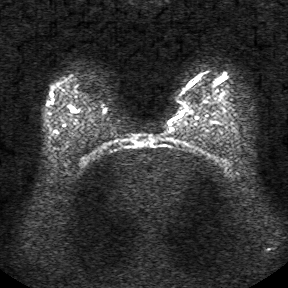
Breast MRI, one axial slice; diffusion-weighted series; image 2 of 4 stored at this slice position (different b-values; order by instance number); 1.5 T; 5 mm slice thickness; 288 × 288 image matrix, field of view 340 × 340 mm. Female patient.
Outlined on this slice (manually delineated by an expert):
- tumour on diffusion-weighted imaging: bounding box (x1, y1, x2, y2) in pixels: (70, 108, 77, 113)